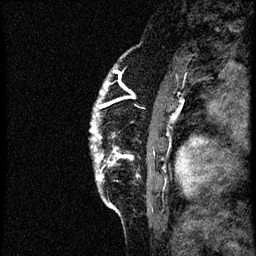
Breast MRI (dynamic contrast-enhanced), one sagittal slice; slice 8 of 56 in the series (ordered by position); dynamic contrast-enhanced study with each time point stored as its own series, time point 2 of 3 at this slice position (early post-contrast, ordered by acquisition time); 1.5 T; TE 4.2 ms, TR 21.3 ms; 2 mm slice thickness; 256 × 256 image matrix, field of view 200 × 200 mm. Female patient, age 41 years. From the clinical record (not read from this slice): setting: breast cancer imaged before/during neoadjuvant chemotherapy; receptor status: HER2-positive.
Structures marked on this image (semi-automatically segmented with operator editing):
- analysis volume of interest (the breast-tissue region the enhancement analysis was run in; not a lesion): bounding box <89,73,177,205> (left, top, right, bottom; pixels)
- tumour enhancement mask (voxels above the 100 % enhancement threshold inside the analysis volume of interest): <90,84,119,155>